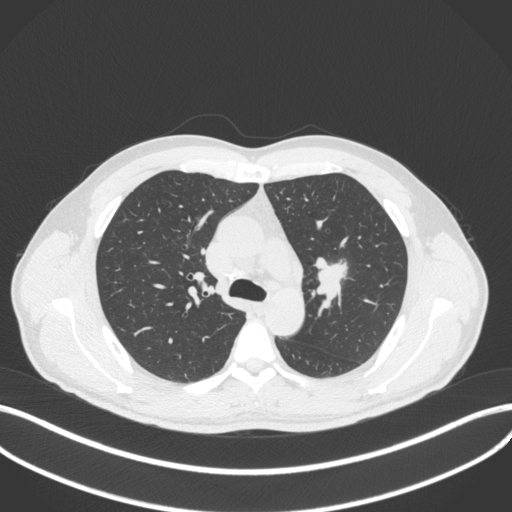
Chest CT, one axial slice. Slice 285 of 383 in the series (ordered by position). Reconstruction kernel B31f. 120 kVp. Lung window (W 1500 / L -600 HU). 1 mm slice thickness. 512 × 512 image matrix, field of view 400 × 400 mm. Patient: male, 50 years. Case-level facts recorded for this patient, not image findings: clinical TNM (as recorded): T1c N1 M1b.
Annotated regions visible in this slice (rectangle marked by the reading radiologist):
- lung tumour (recorded histology: squamous cell carcinoma): bounding box (x1, y1, x2, y2) in pixels: (312, 253, 351, 298)